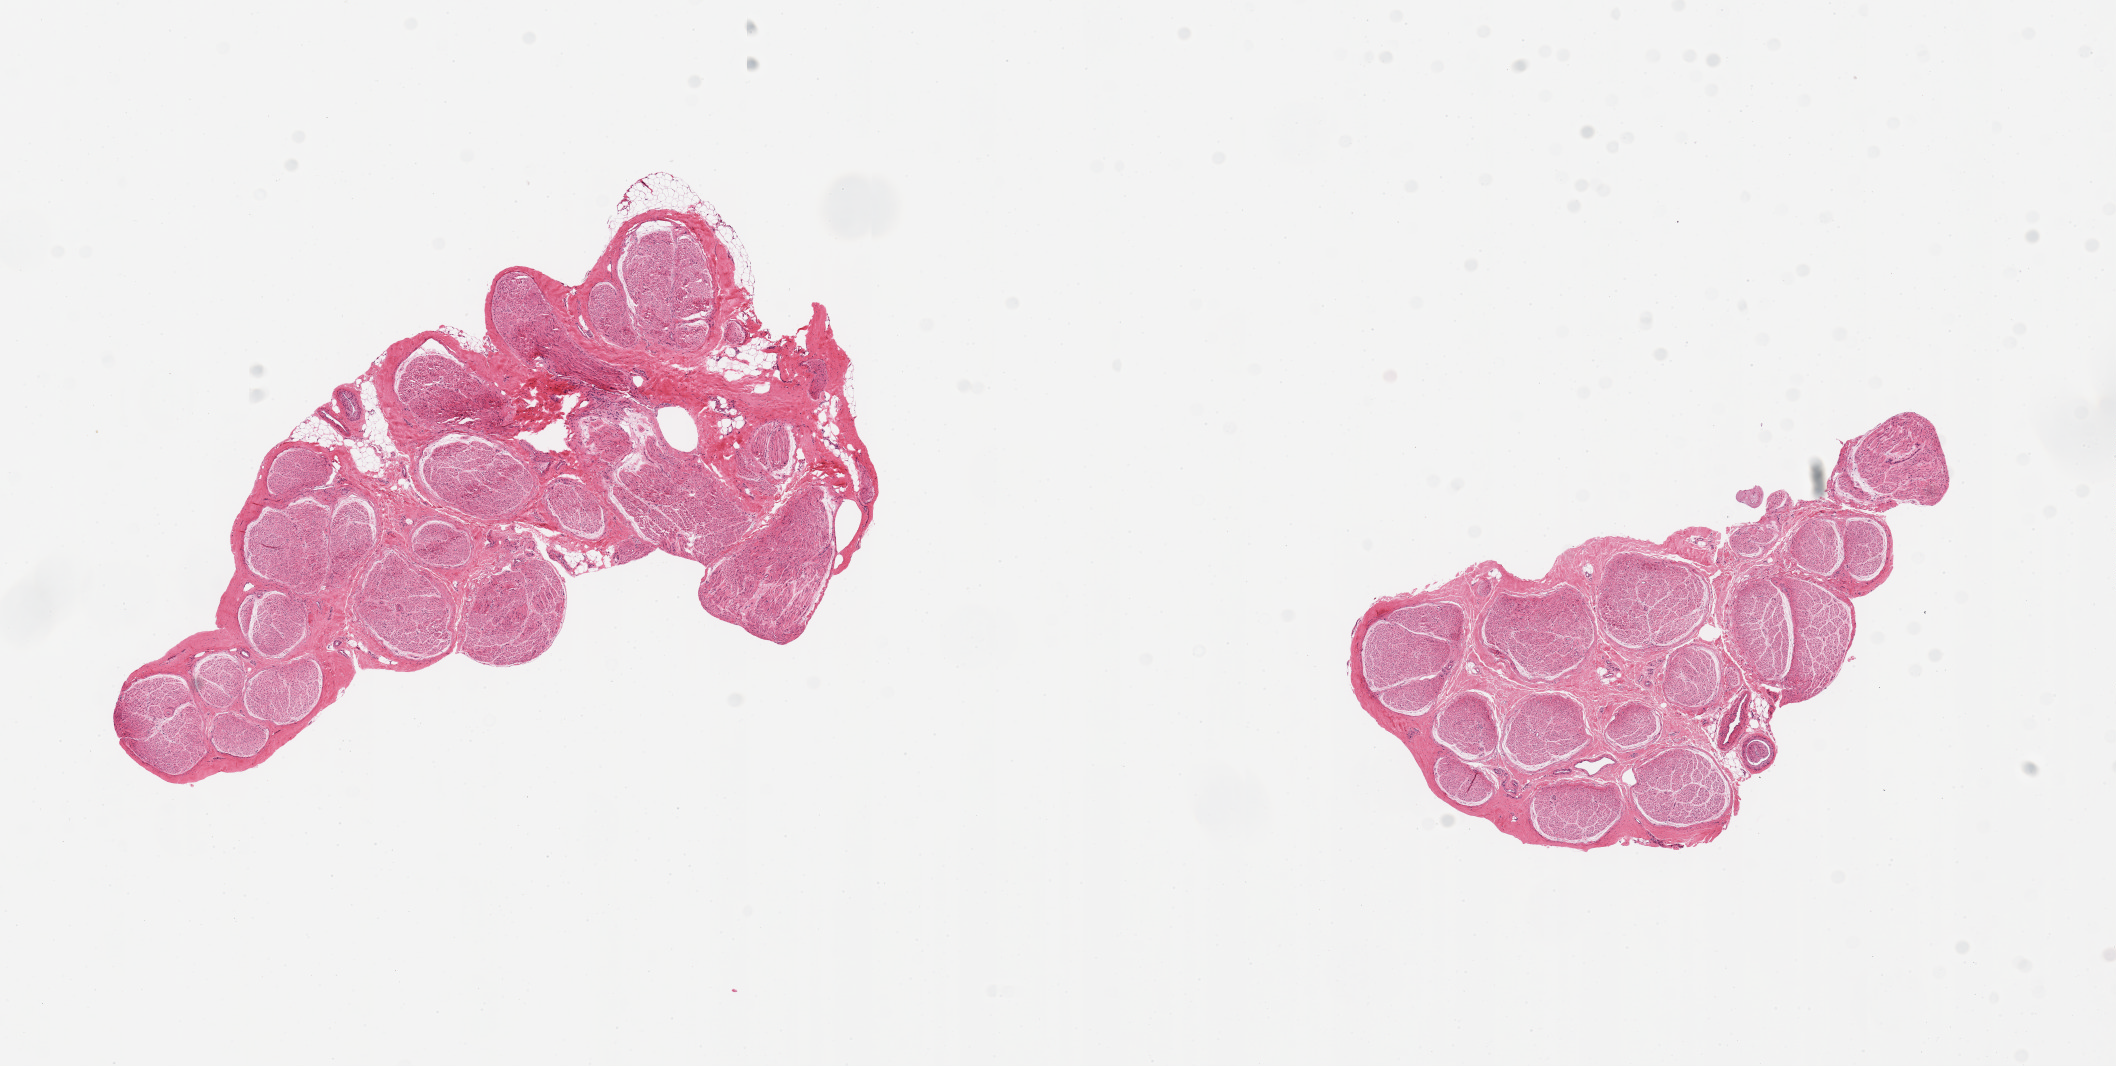
Whole-slide image, haematoxylin and eosin stain, a low-resolution overview of the entire scanned area, about 16.7 x 8.4 mm (acquisition: 20x scan); PAXgene-fixed, paraffin-embedded tissue; sampled site (target tissue): tibial nerve; donor tissue sample. Female donor.
• pathologist's review note for this sample: 2 pieces